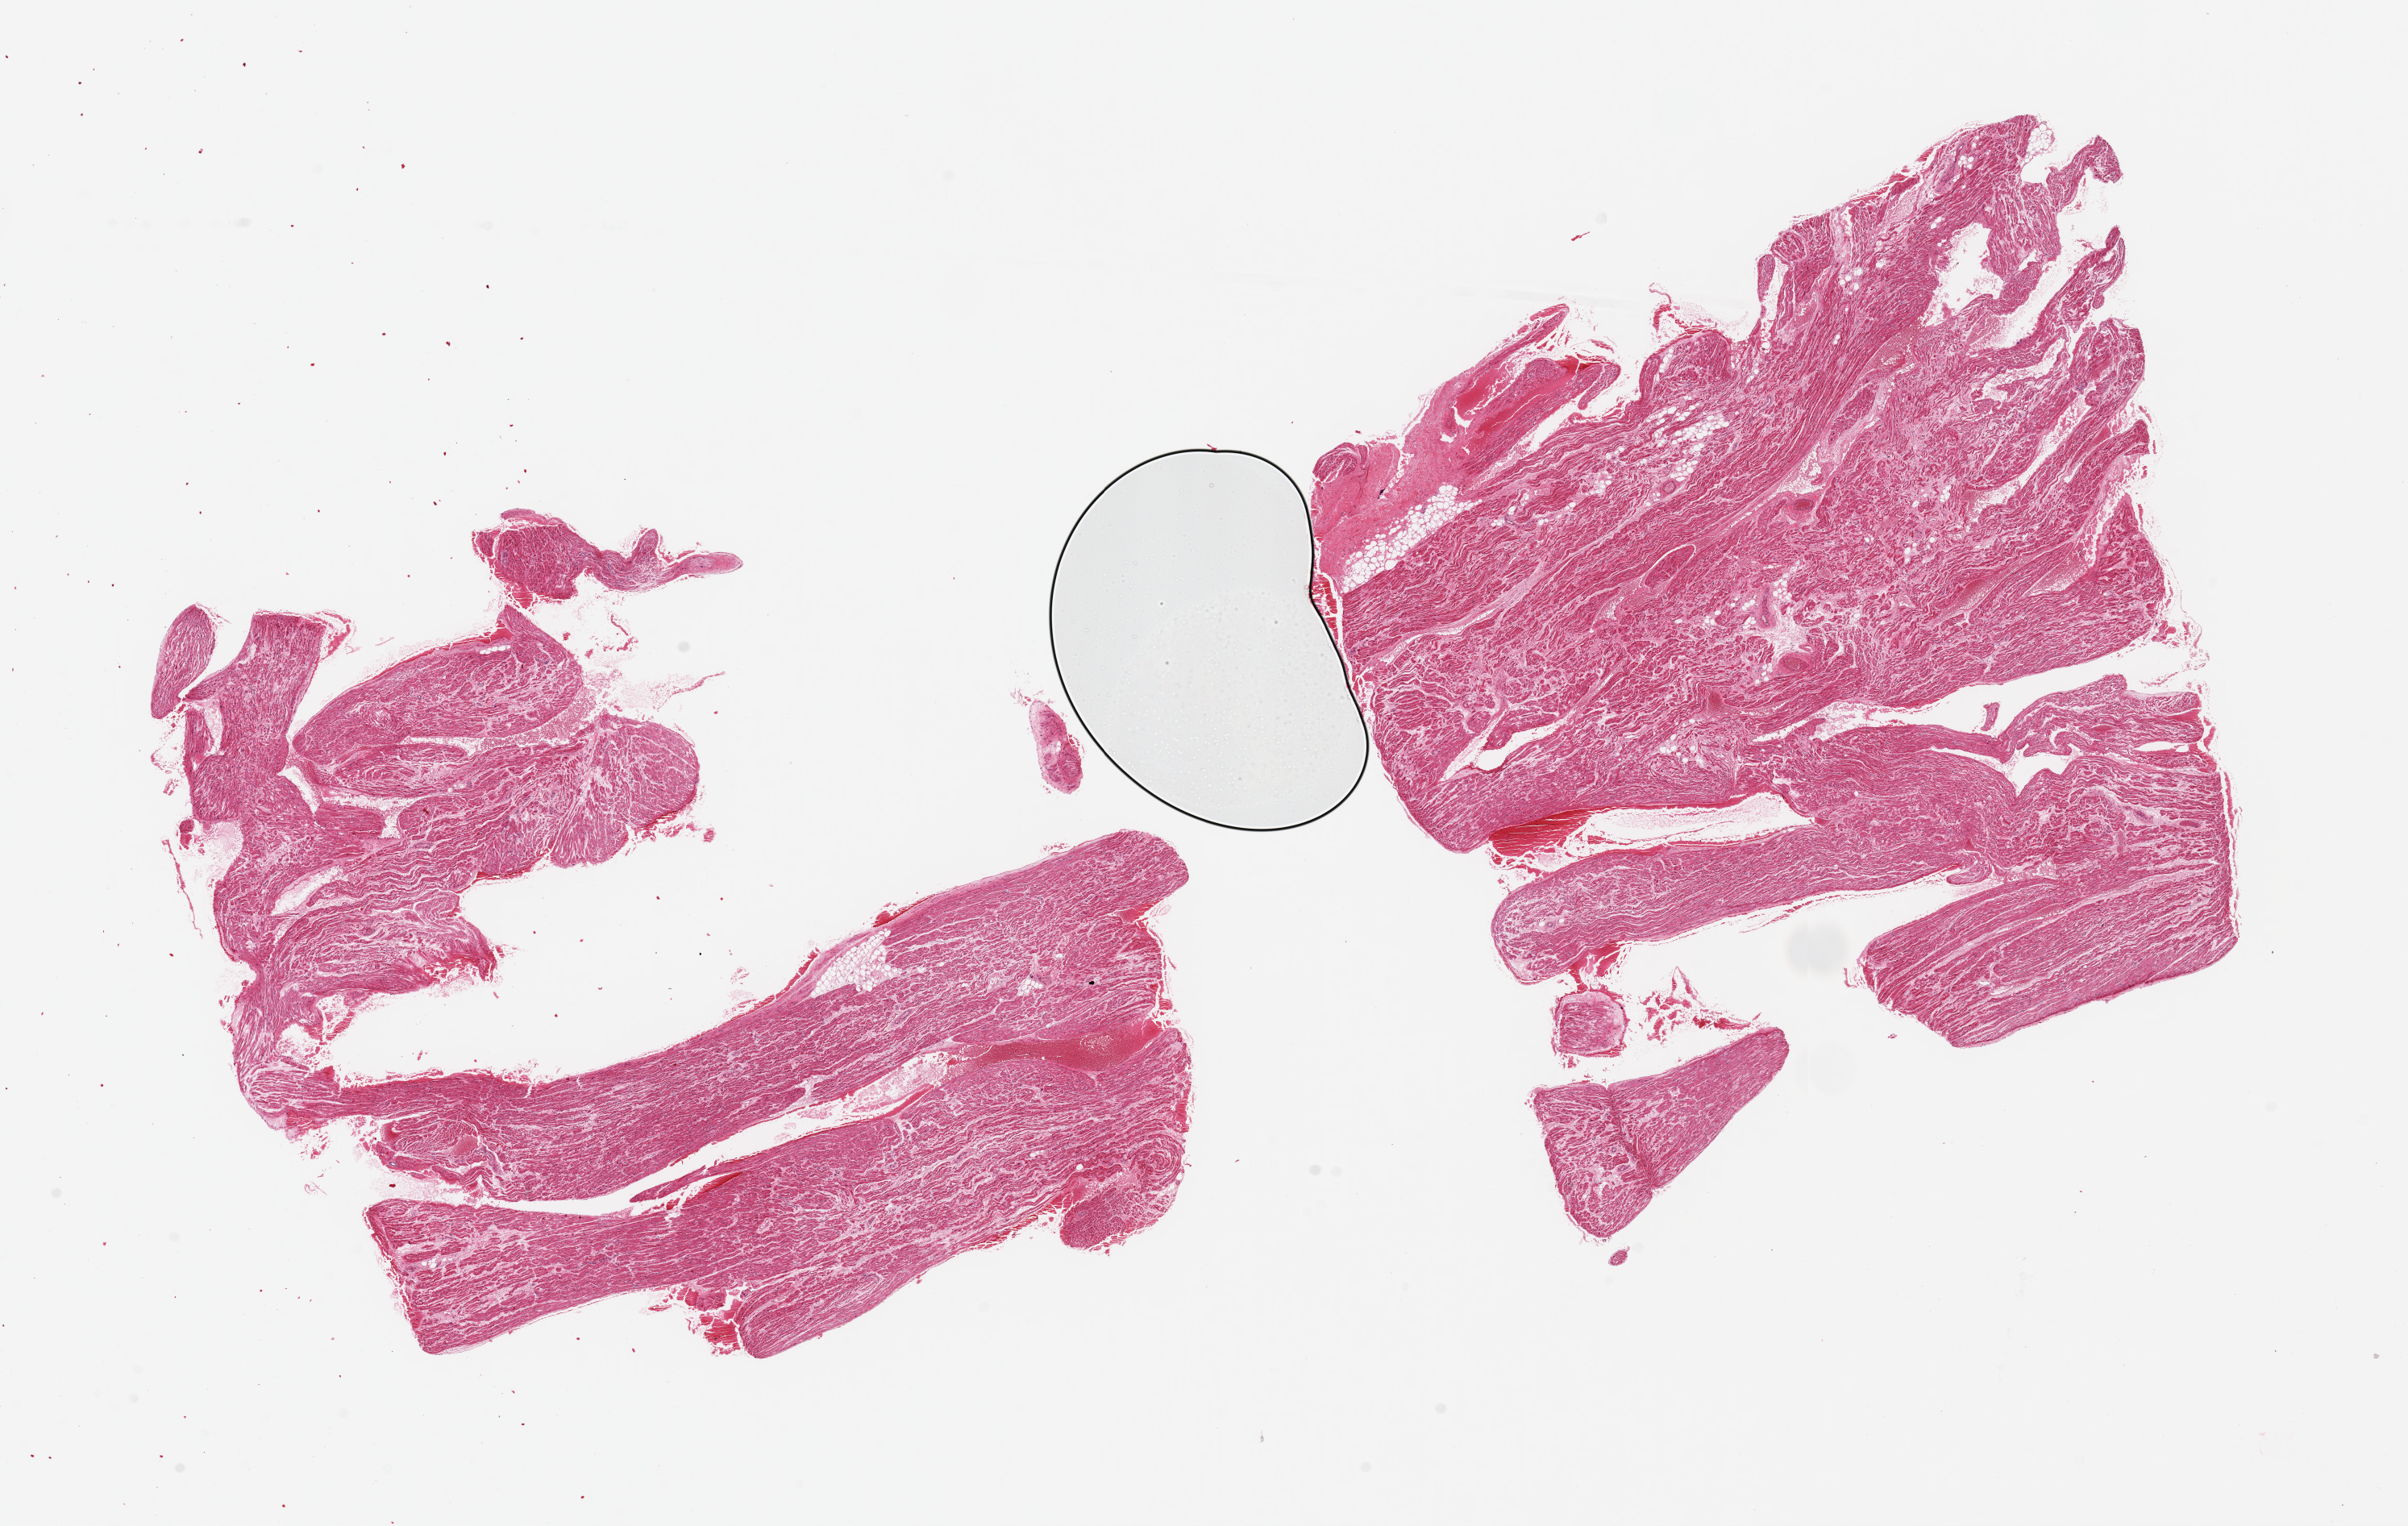
Whole-slide image, hematoxylin and eosin (H&E) stain, brightfield, a low-resolution overview of the entire scanned area, about 23.6 x 15.0 mm; PAXgene-fixed paraffin-embedded (PFPE) section; sampled site (target tissue): auricular appendage; tissue donor sample.
Pathologist's review note for this sample: 2 pieces, 9x9 & 9x9mm.